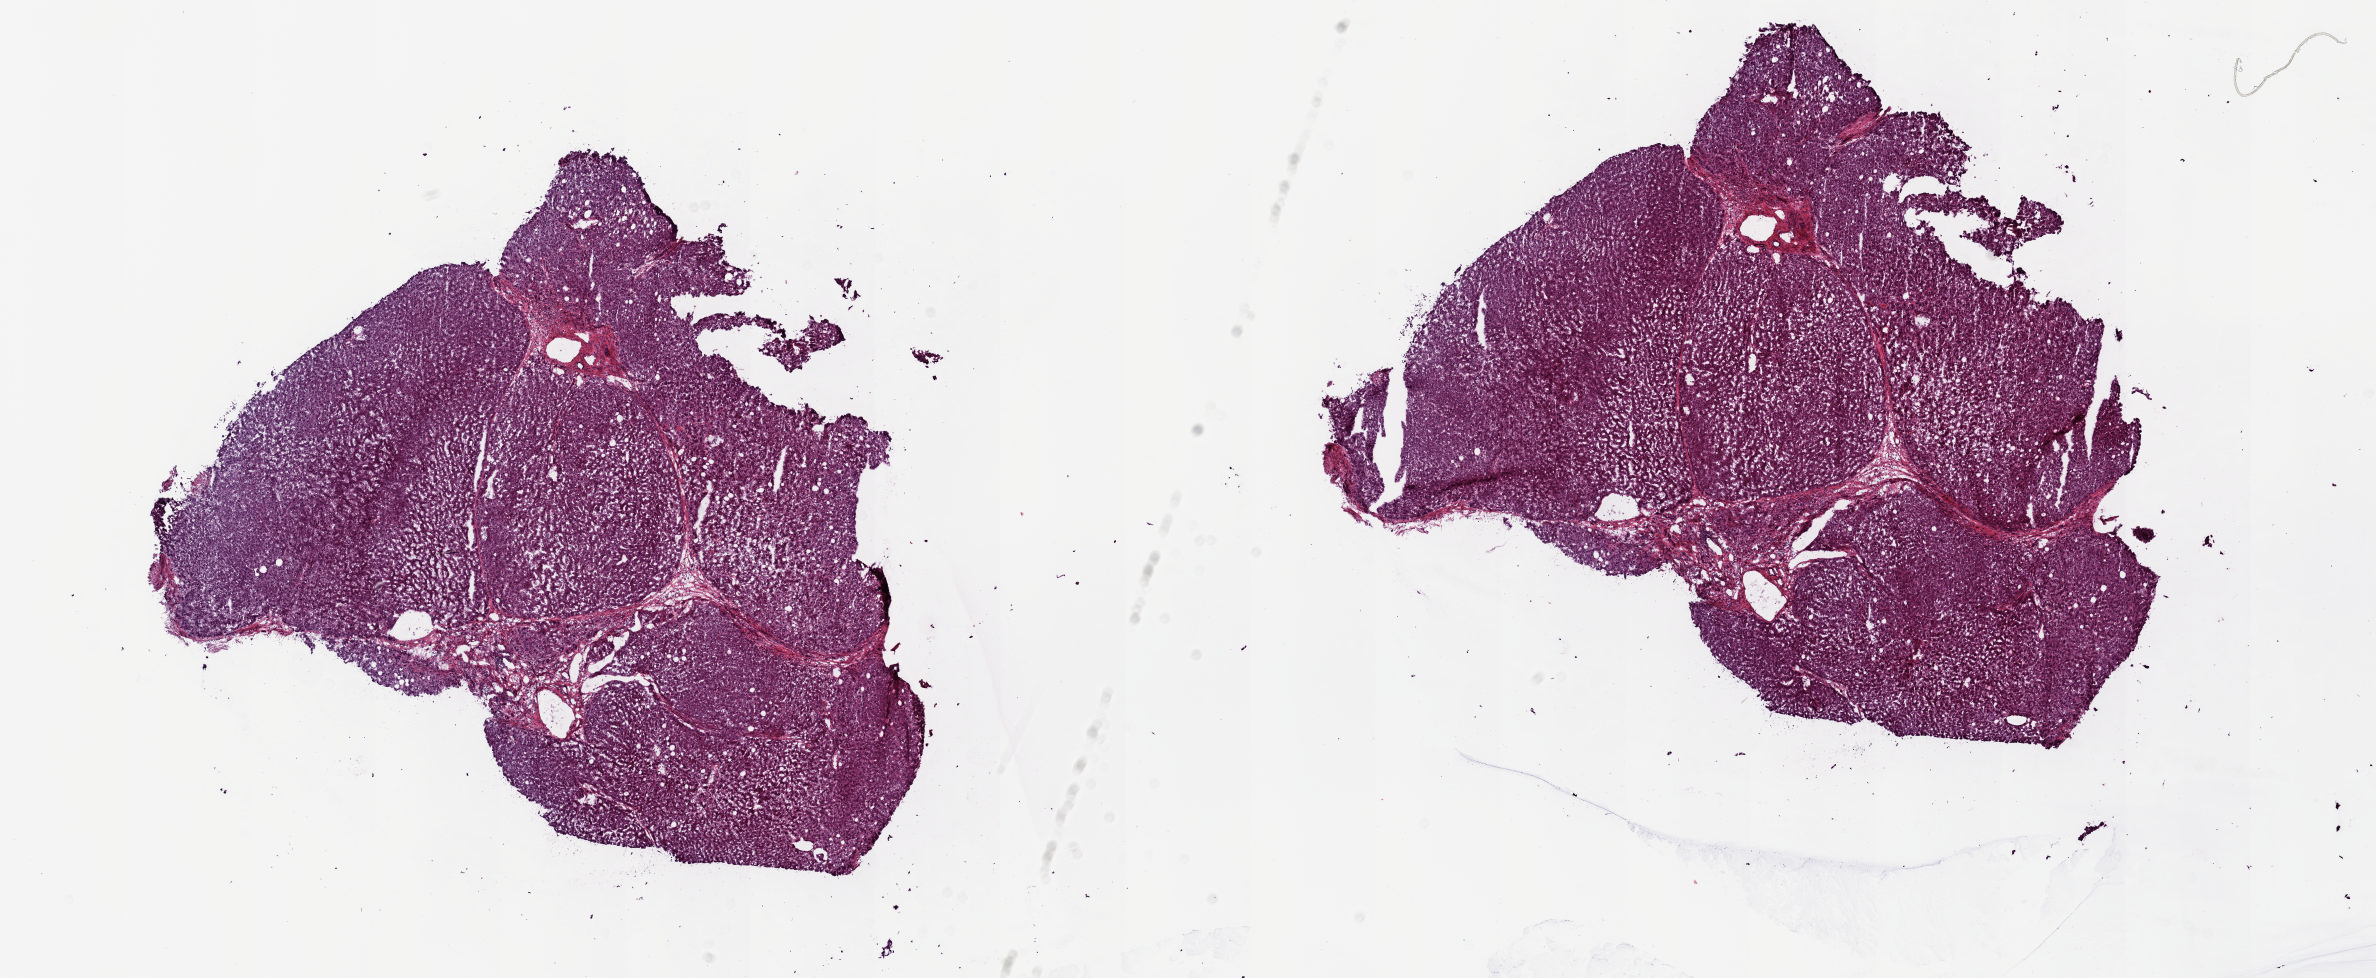
Whole-slide histology image, H&E — shown as a low-resolution overview of the whole scanned area (about 18.8 x 7.8 mm, acquisition: 20x scan). Frozen section from the top of the tissue portion. Liver, solid tissue normal (non-tumour tissue) sample. Patient: male, age at initial diagnosis 70 years. Composition of this section per pathologist review: tumour cells 0%, tumour nuclei 0%, normal cells 100%, stromal cells 0%, necrosis 0%. Inflammatory infiltration, as recorded: lymphocyte infiltration 0%, monocyte infiltration 0%, neutrophil infiltration 0%.
This section: solid tissue normal sample (biorepository sample class). Patient diagnosis: Hepatocellular carcinoma, NOS.